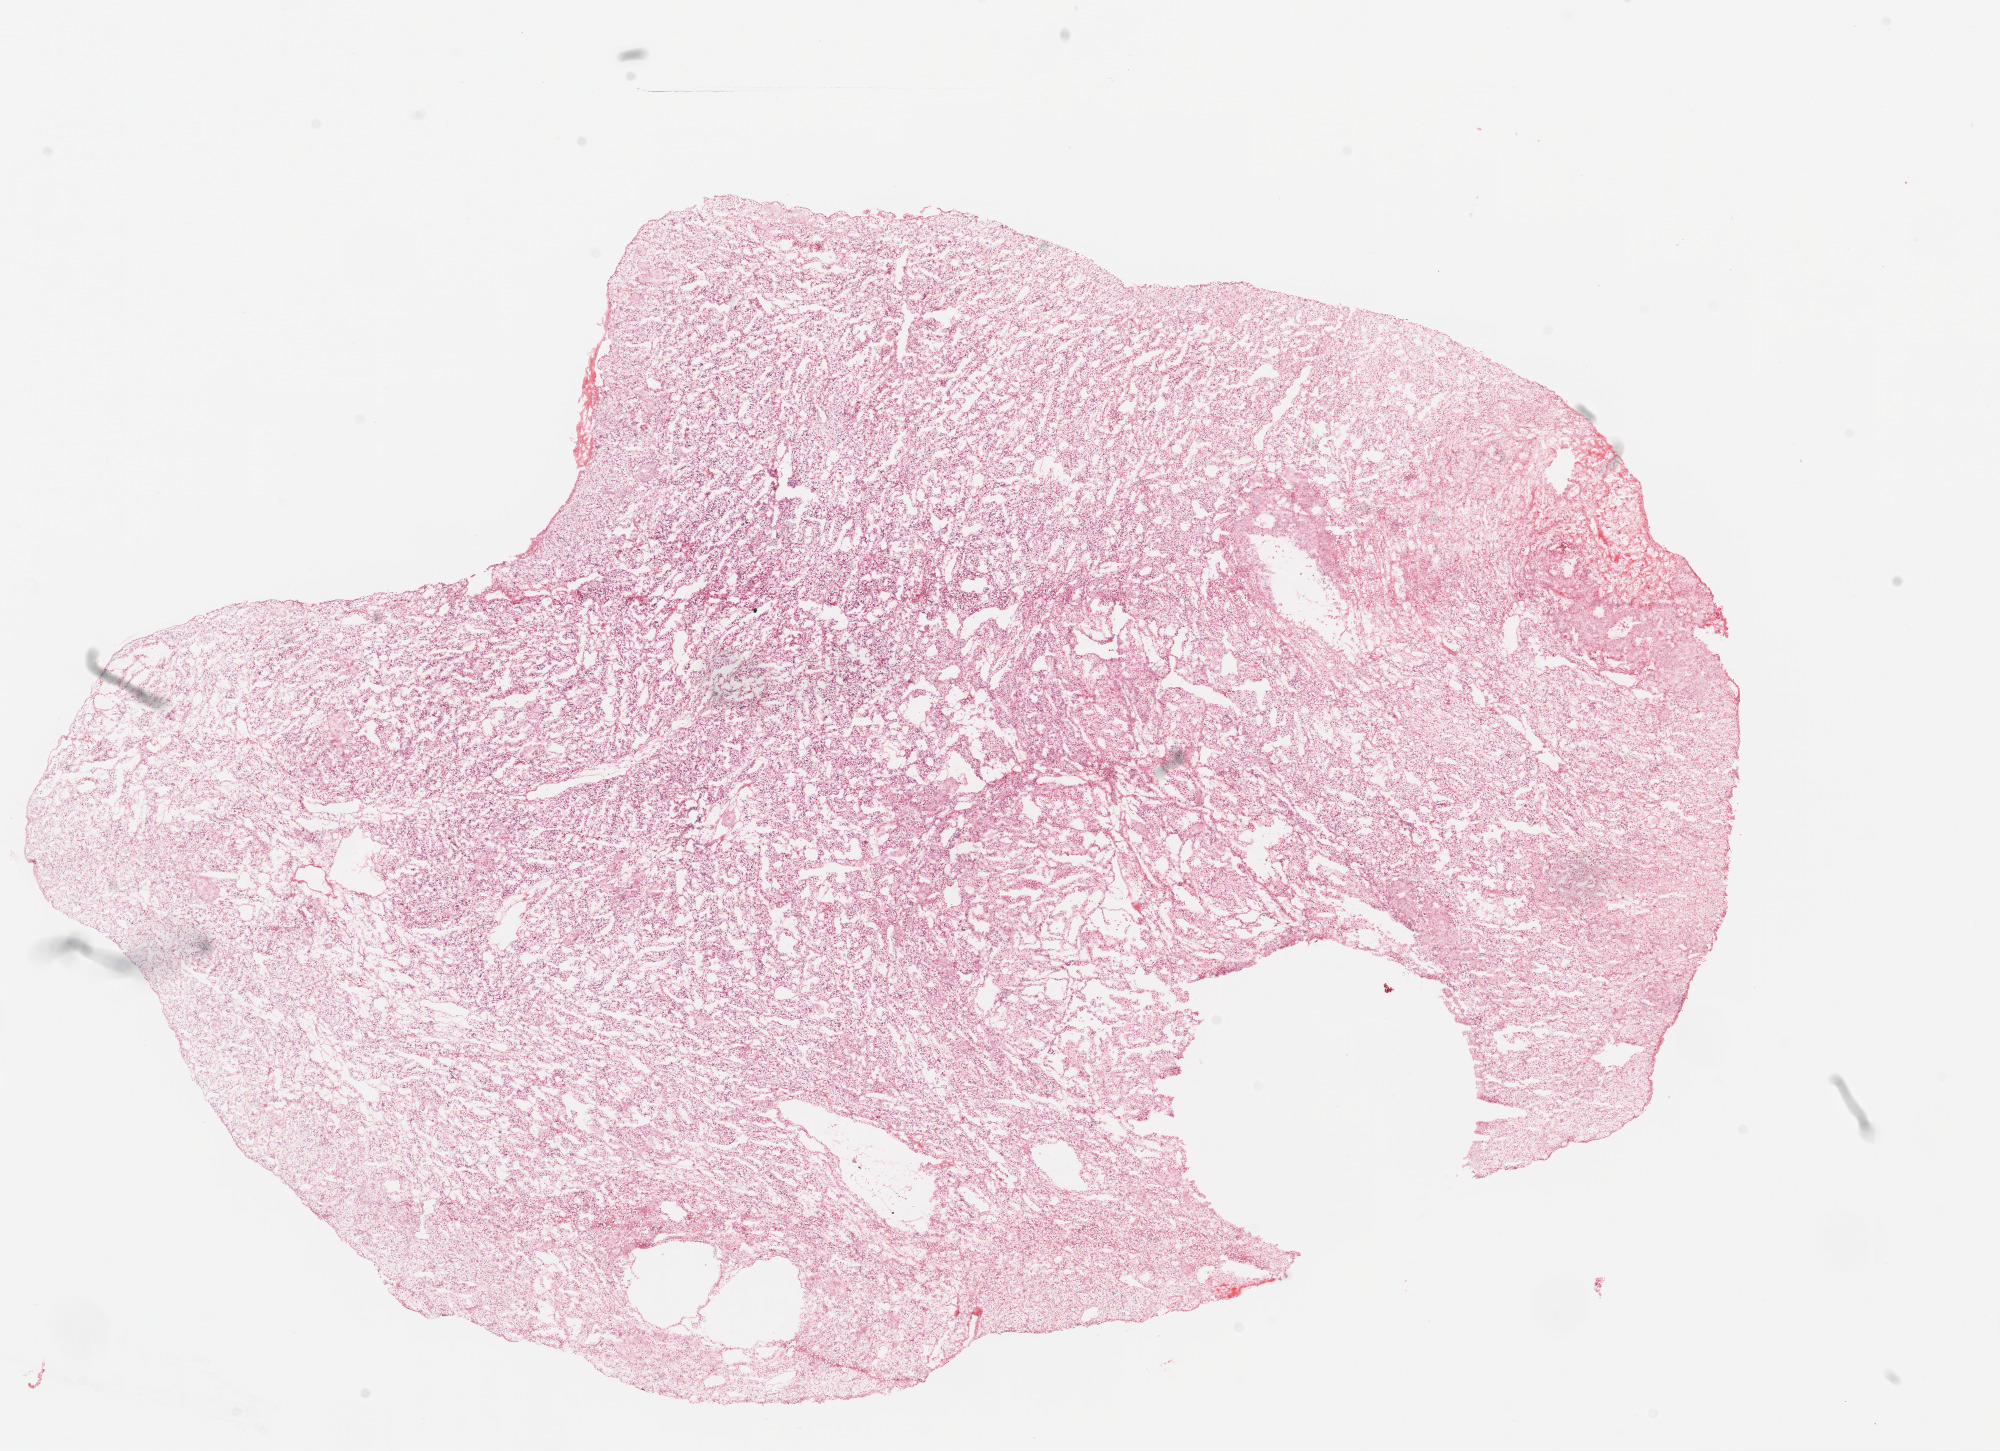
Whole-slide histology image, H&E-stained — a low-resolution overview of the entire scanned area, about 16.0 x 11.6 mm (acquisition: 20x scan), frozen section from the top of the tissue portion, primary tumour sample from the kidney. Male, age 63 years at initial diagnosis. Histologic grade: G4 (undifferentiated). Pathologist review of this section (percent, as recorded): tumour cells 95%, tumour nuclei 90%, normal cells 0%, stromal cells 5%, necrosis 0%. Infiltration values recorded for this section: lymphocyte infiltration 2%, monocyte infiltration 0%, neutrophil infiltration 0%.
Pathologic diagnosis: Clear cell adenocarcinoma, NOS. Laterality: right. AJCC pathologic stage: IV.